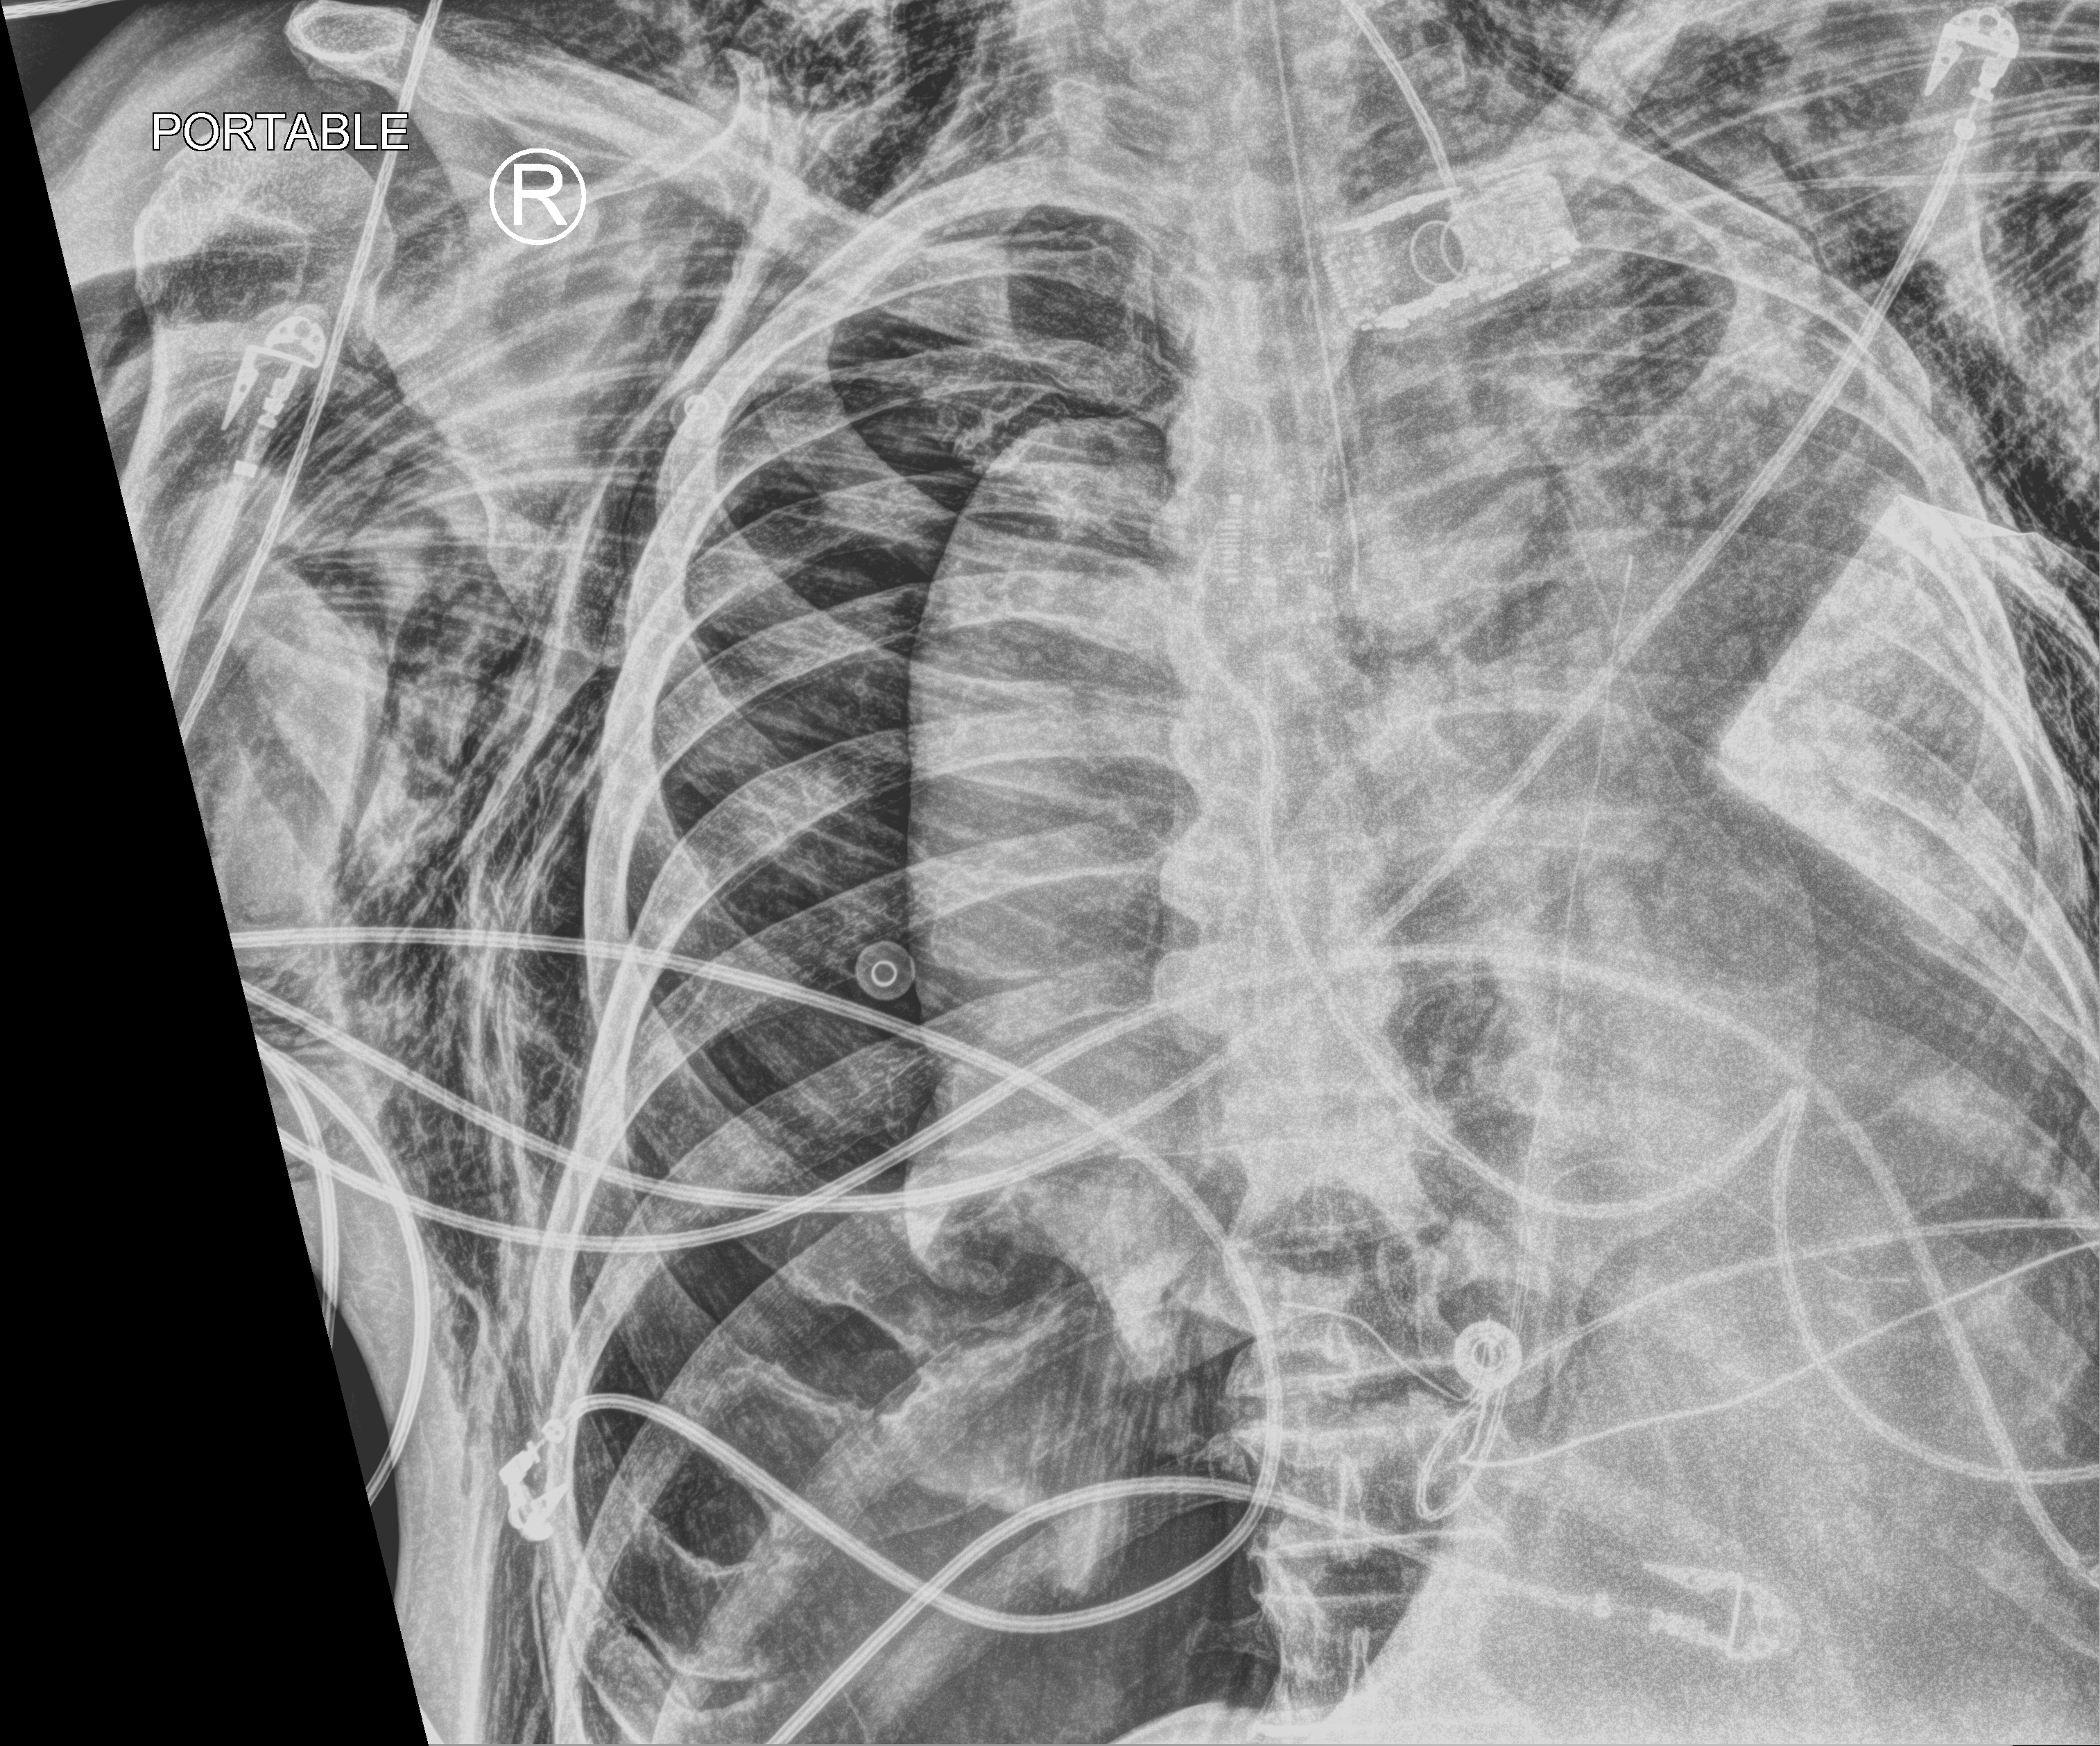
Portable chest radiograph; anteroposterior (AP) projection. Patient hospitalised with COVID-19; male, aged 75–90 years.
From the hospital-stay record, not from the radiograph (when in the stay this image was taken is not recorded): admitted to intensive care during this hospital stay: yes; mechanically ventilated during this hospital stay: yes.